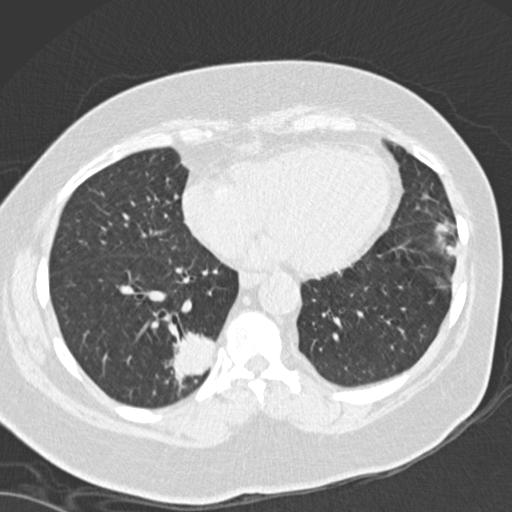
Low-dose screening chest CT, axial slice; baseline screening round; lung window (W 1500 / L -600 HU); slice 106 of 162 in the series. Female, age 66 years at enrolment. Current smoker at enrolment.
Expert reader's lesion annotation, box from (x=145, y=315) to (x=233, y=407) px. The screening reader recorded 3 non-calcified nodules or masses ≥4 mm on this exam (left lower lobe, left lower lobe, right lower lobe); which of them this box marks is not recorded. Lung cancer was diagnosed 67 days after this screen: adenocarcinoma, NOS, right lower lobe, well differentiated (G1), stage IB (AJCC 6th edition), 55 mm at pathology.